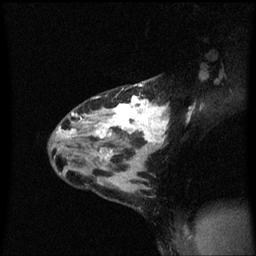
Breast MRI (dynamic contrast-enhanced), one sagittal slice. Position 38 of 60 along the scan axis. Dynamic contrast-enhanced series, image 2 of 3 at this slice position (ordered by acquisition). 1.5 T. TE 4.2 ms, TR 8.4 ms. 256 × 256 image matrix, field of view 200 × 200 mm. Female patient, age 32 years.
Outlined on this slice (semi-automatically segmented with operator editing):
- analysis volume of interest (the breast-tissue region the enhancement analysis was run in; not a lesion): bounding box (x1, y1, x2, y2) in pixels: (55, 78, 171, 167)
- tumour enhancement mask (voxels above the 70 % enhancement threshold inside the analysis volume of interest): (57, 84, 170, 159)